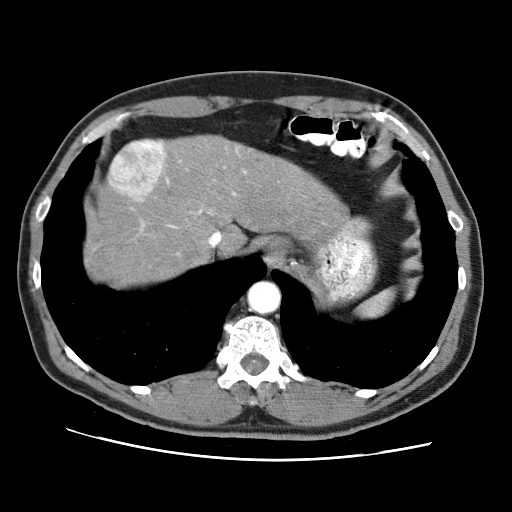
Contrast-enhanced abdominal CT (liver protocol), one axial slice; position 58 of 71 along the scan axis; 120 kVp; soft-tissue window (W 400 / L 40 HU); 2.5 mm slice thickness; 512 × 512 image matrix, field of view 360 × 360 mm. From the clinical record (not read from this slice): diagnosis: hepatocellular carcinoma (patient treated with transarterial chemoembolisation; whether this scan precedes or follows treatment is not stated here); TNM stage (as recorded): Stage-II; Child-Pugh class: A; tumour differentiation: well differentiated; tumour nodularity: multinodular.
Outlined on this slice (semi-automatic segmentation, software-assisted and operator-edited):
- liver parenchyma outside the tumour (the mass and vessels are separate outlines, so this box may not span the whole liver): bounding box (x1, y1, x2, y2) in pixels: (86, 134, 347, 285)
- mass: (106, 141, 166, 204)
- liver vessels: (166, 180, 235, 227)